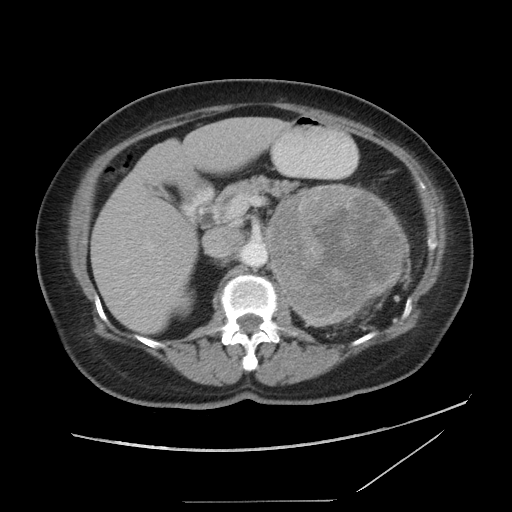
Contrast-enhanced abdominal CT, one axial slice; position 55 of 86 along the scan axis; reconstruction kernel STANDARD; 120 kVp; soft-tissue window (W 400 / L 40 HU); 5 mm slice thickness; 512 × 512 image matrix. Female patient, age 77 years. Case-level facts recorded for this patient, not image findings: diagnosis: adrenocortical carcinoma; tumour side: left adrenal; tumour size at pathology: 13.1 cm; Ki-67 index: 10 %; stage (as recorded): 3.
Outlined on this slice (semi-automatic segmentation, software-assisted and operator-edited):
- mass: bounding box [x1, y1, x2, y2] px = [268, 185, 407, 325]